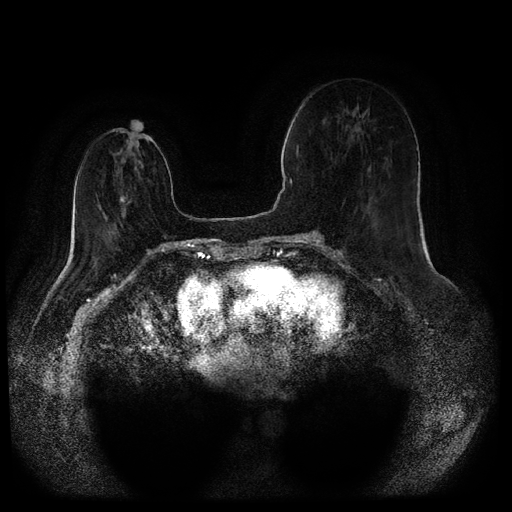
Breast MRI (dynamic contrast-enhanced, multi-phase), one axial slice. Position 29 of 116 along the scan axis. Dynamic contrast-enhanced series, time point 2 of 5 at this slice position (early post-contrast). 1.5 T. TE 2.6 ms, TR 5.3 ms. 512 × 512 image matrix, field of view 360 × 360 mm. Patient: female, 71 years.
Outlined on this slice (semi-automatically segmented with operator editing):
- breast lesion (labelled 'tumour' in the annotation; benign lesions carry a separate 'benign' label): box from (x=120, y=192) to (x=126, y=204) px